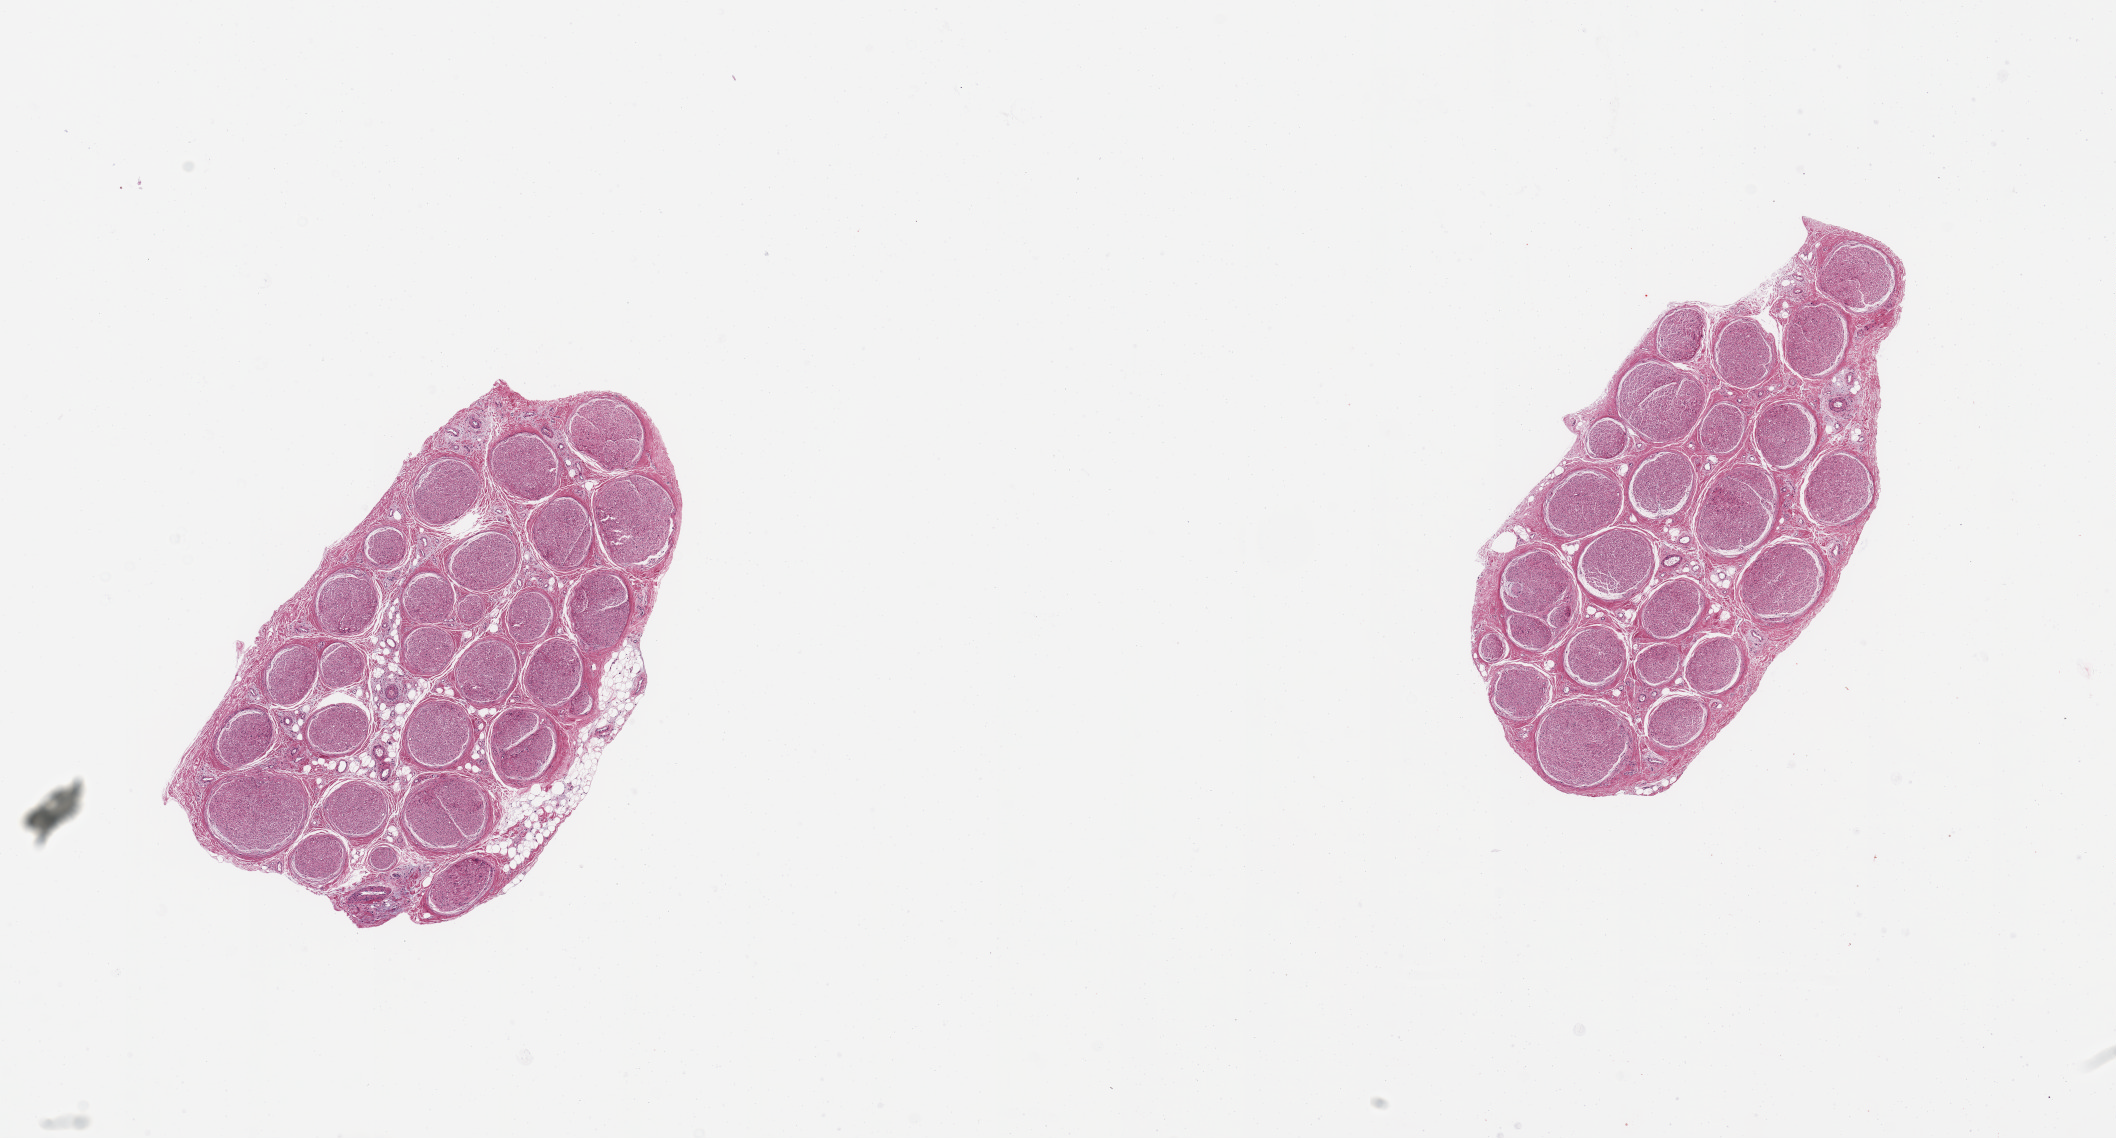
Haematoxylin and eosin whole-slide image, brightfield, whole scanned area (about 16.7 x 9.0 mm) shown as a low-resolution overview; PAXgene-fixed paraffin-embedded (PFPE) section; target tissue: tibial nerve; donor tissue sample. Female donor.
- reviewer comment on this tissue sample: 2 pieces, peripheral nerve, no adherent fat